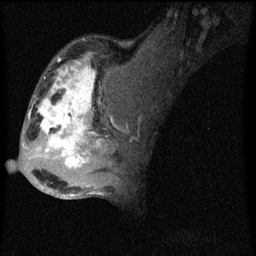
Breast MRI (dynamic contrast-enhanced), one sagittal slice. Dynamic contrast-enhanced series, image 2 of 4 at this slice position (ordered by acquisition). 1.5 T. TE 4.2 ms, TR 8 ms. 2 mm slice thickness. 256 × 256 image matrix. Female patient, age 50 years.
Structures marked on this image (semi-automatically segmented with operator editing):
- analysis volume of interest (the breast-tissue region the enhancement analysis was run in; not a lesion): bounding box <26,44,124,177> (left, top, right, bottom; pixels)
- tumour enhancement mask (voxels above the 70 % enhancement threshold inside the analysis volume of interest): <29,56,114,167>